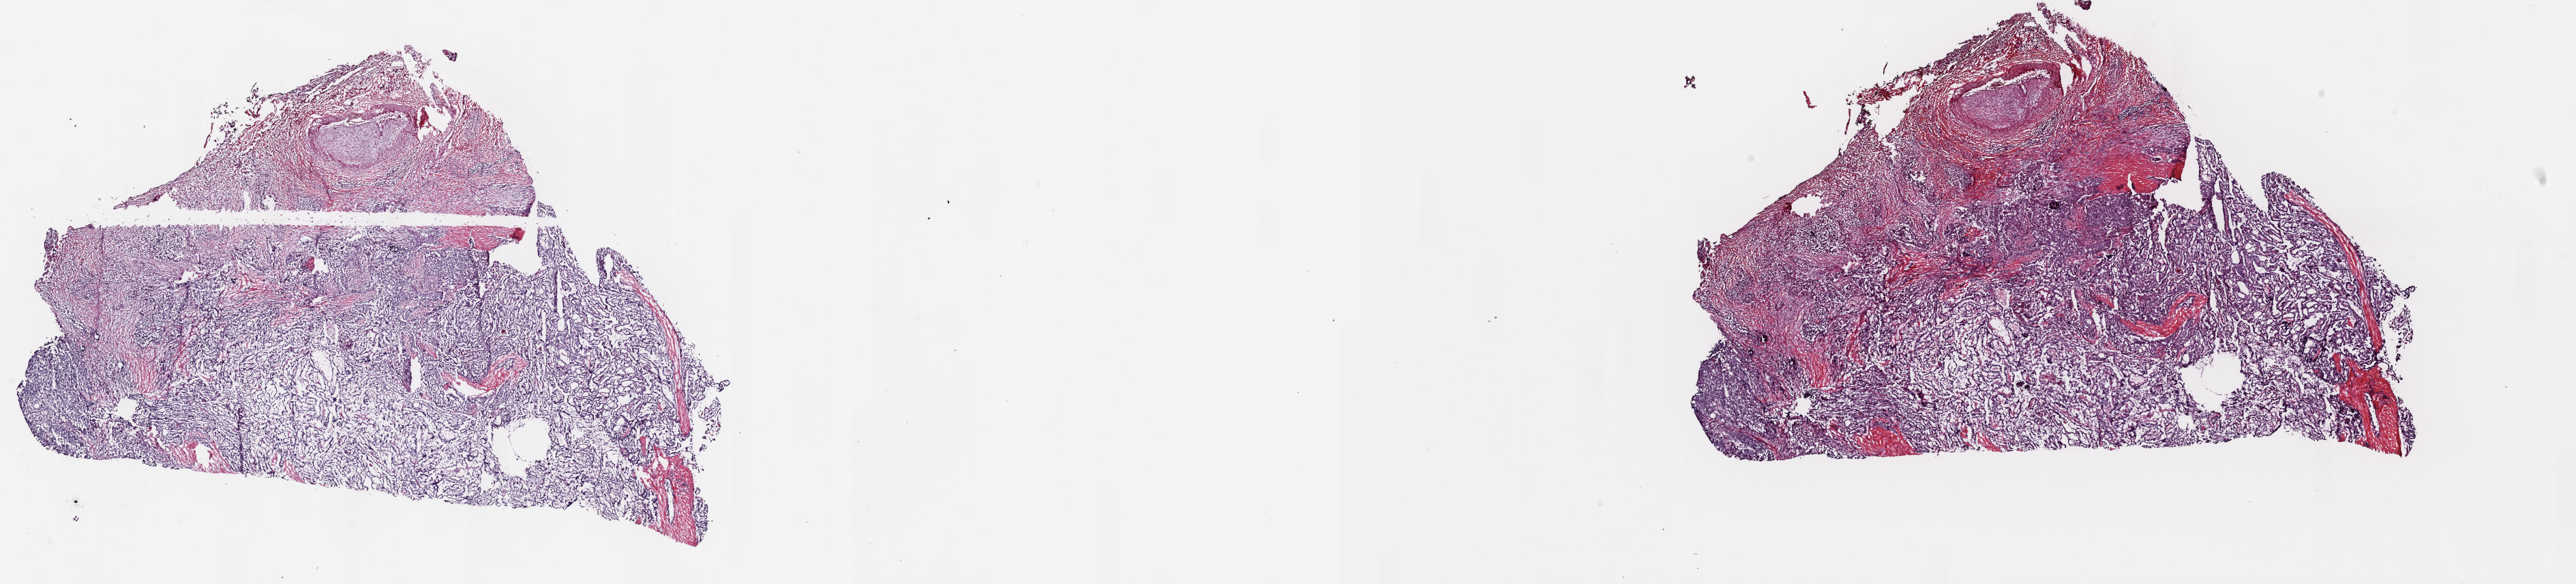
Hematoxylin and eosin (H&E) stained whole-slide image — a low-resolution overview of the entire scanned area, about 29.8 x 6.8 mm; frozen section from the top of the tissue portion; primary tumour sample from the thyroid. Female patient; age at initial diagnosis 24 years. Slide review estimates, as recorded: tumour cells 70%, tumour nuclei 80%, normal cells 0%, stromal cells 30%, necrosis 0%. Inflammatory infiltration, as recorded: lymphocyte infiltration 4%, monocyte infiltration 2%, neutrophil infiltration 0%.
Diagnosis: Papillary adenocarcinoma, NOS (thyroid gland). AJCC pathologic stage: I (6th edition).